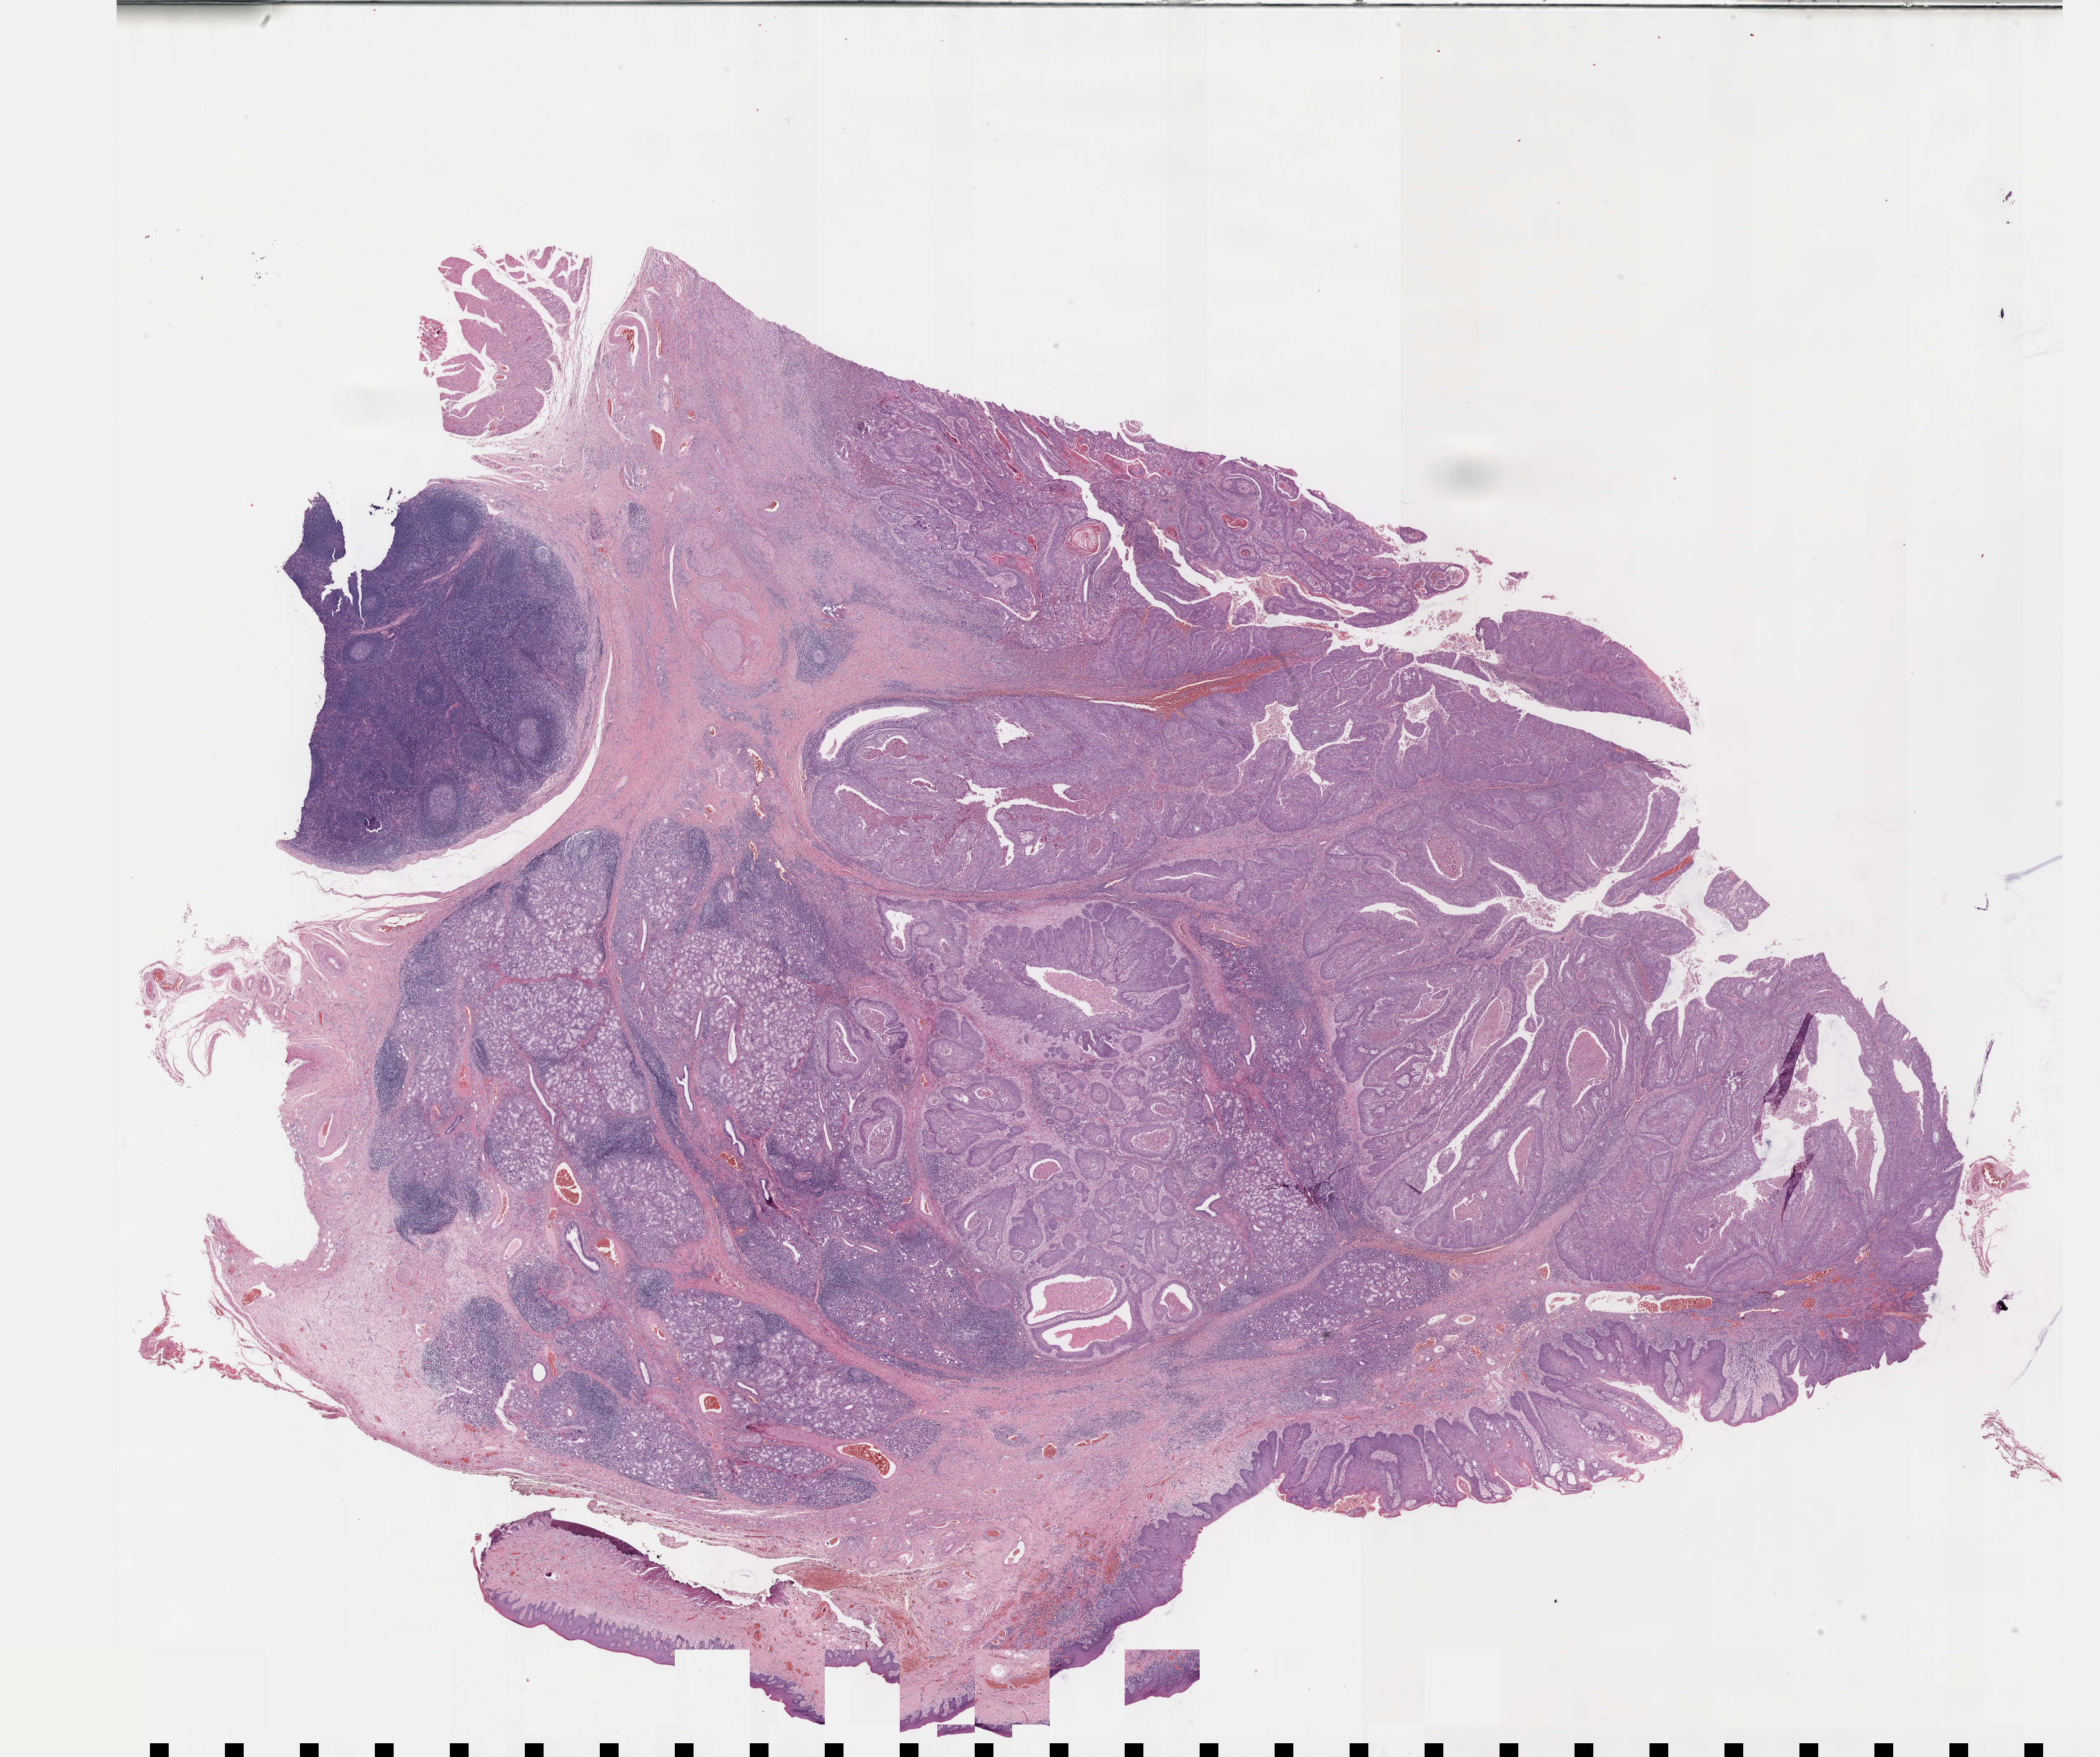
Whole-slide histology image, H&E-stained, shown as a low-resolution overview of the whole scanned area (about 27.2 x 22.7 mm, from a 40x scan); FFPE section; sample: primary tumour, head and neck. Male, age 54 years at initial diagnosis.
Pathologic diagnosis: Squamous cell carcinoma, NOS (floor of mouth, NOS).